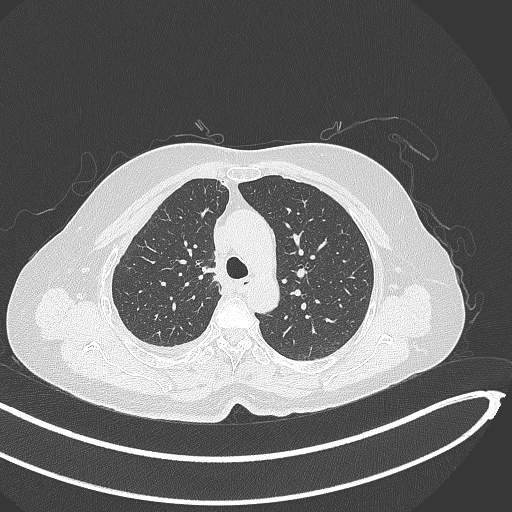
Chest CT, one axial slice; position 268 of 345 along the scan axis; lung window (W 1500 / L -600 HU); 1 mm slice thickness; 512 × 512 image matrix. Patient: female, 64 years. Case-level facts recorded for this patient, not image findings: clinical TNM (as recorded): T1b N0 M1.
Outlined on this slice (bounding box drawn by a radiologist):
- lung tumour (recorded histology: adenocarcinoma): box from (x=200, y=262) to (x=218, y=282) px